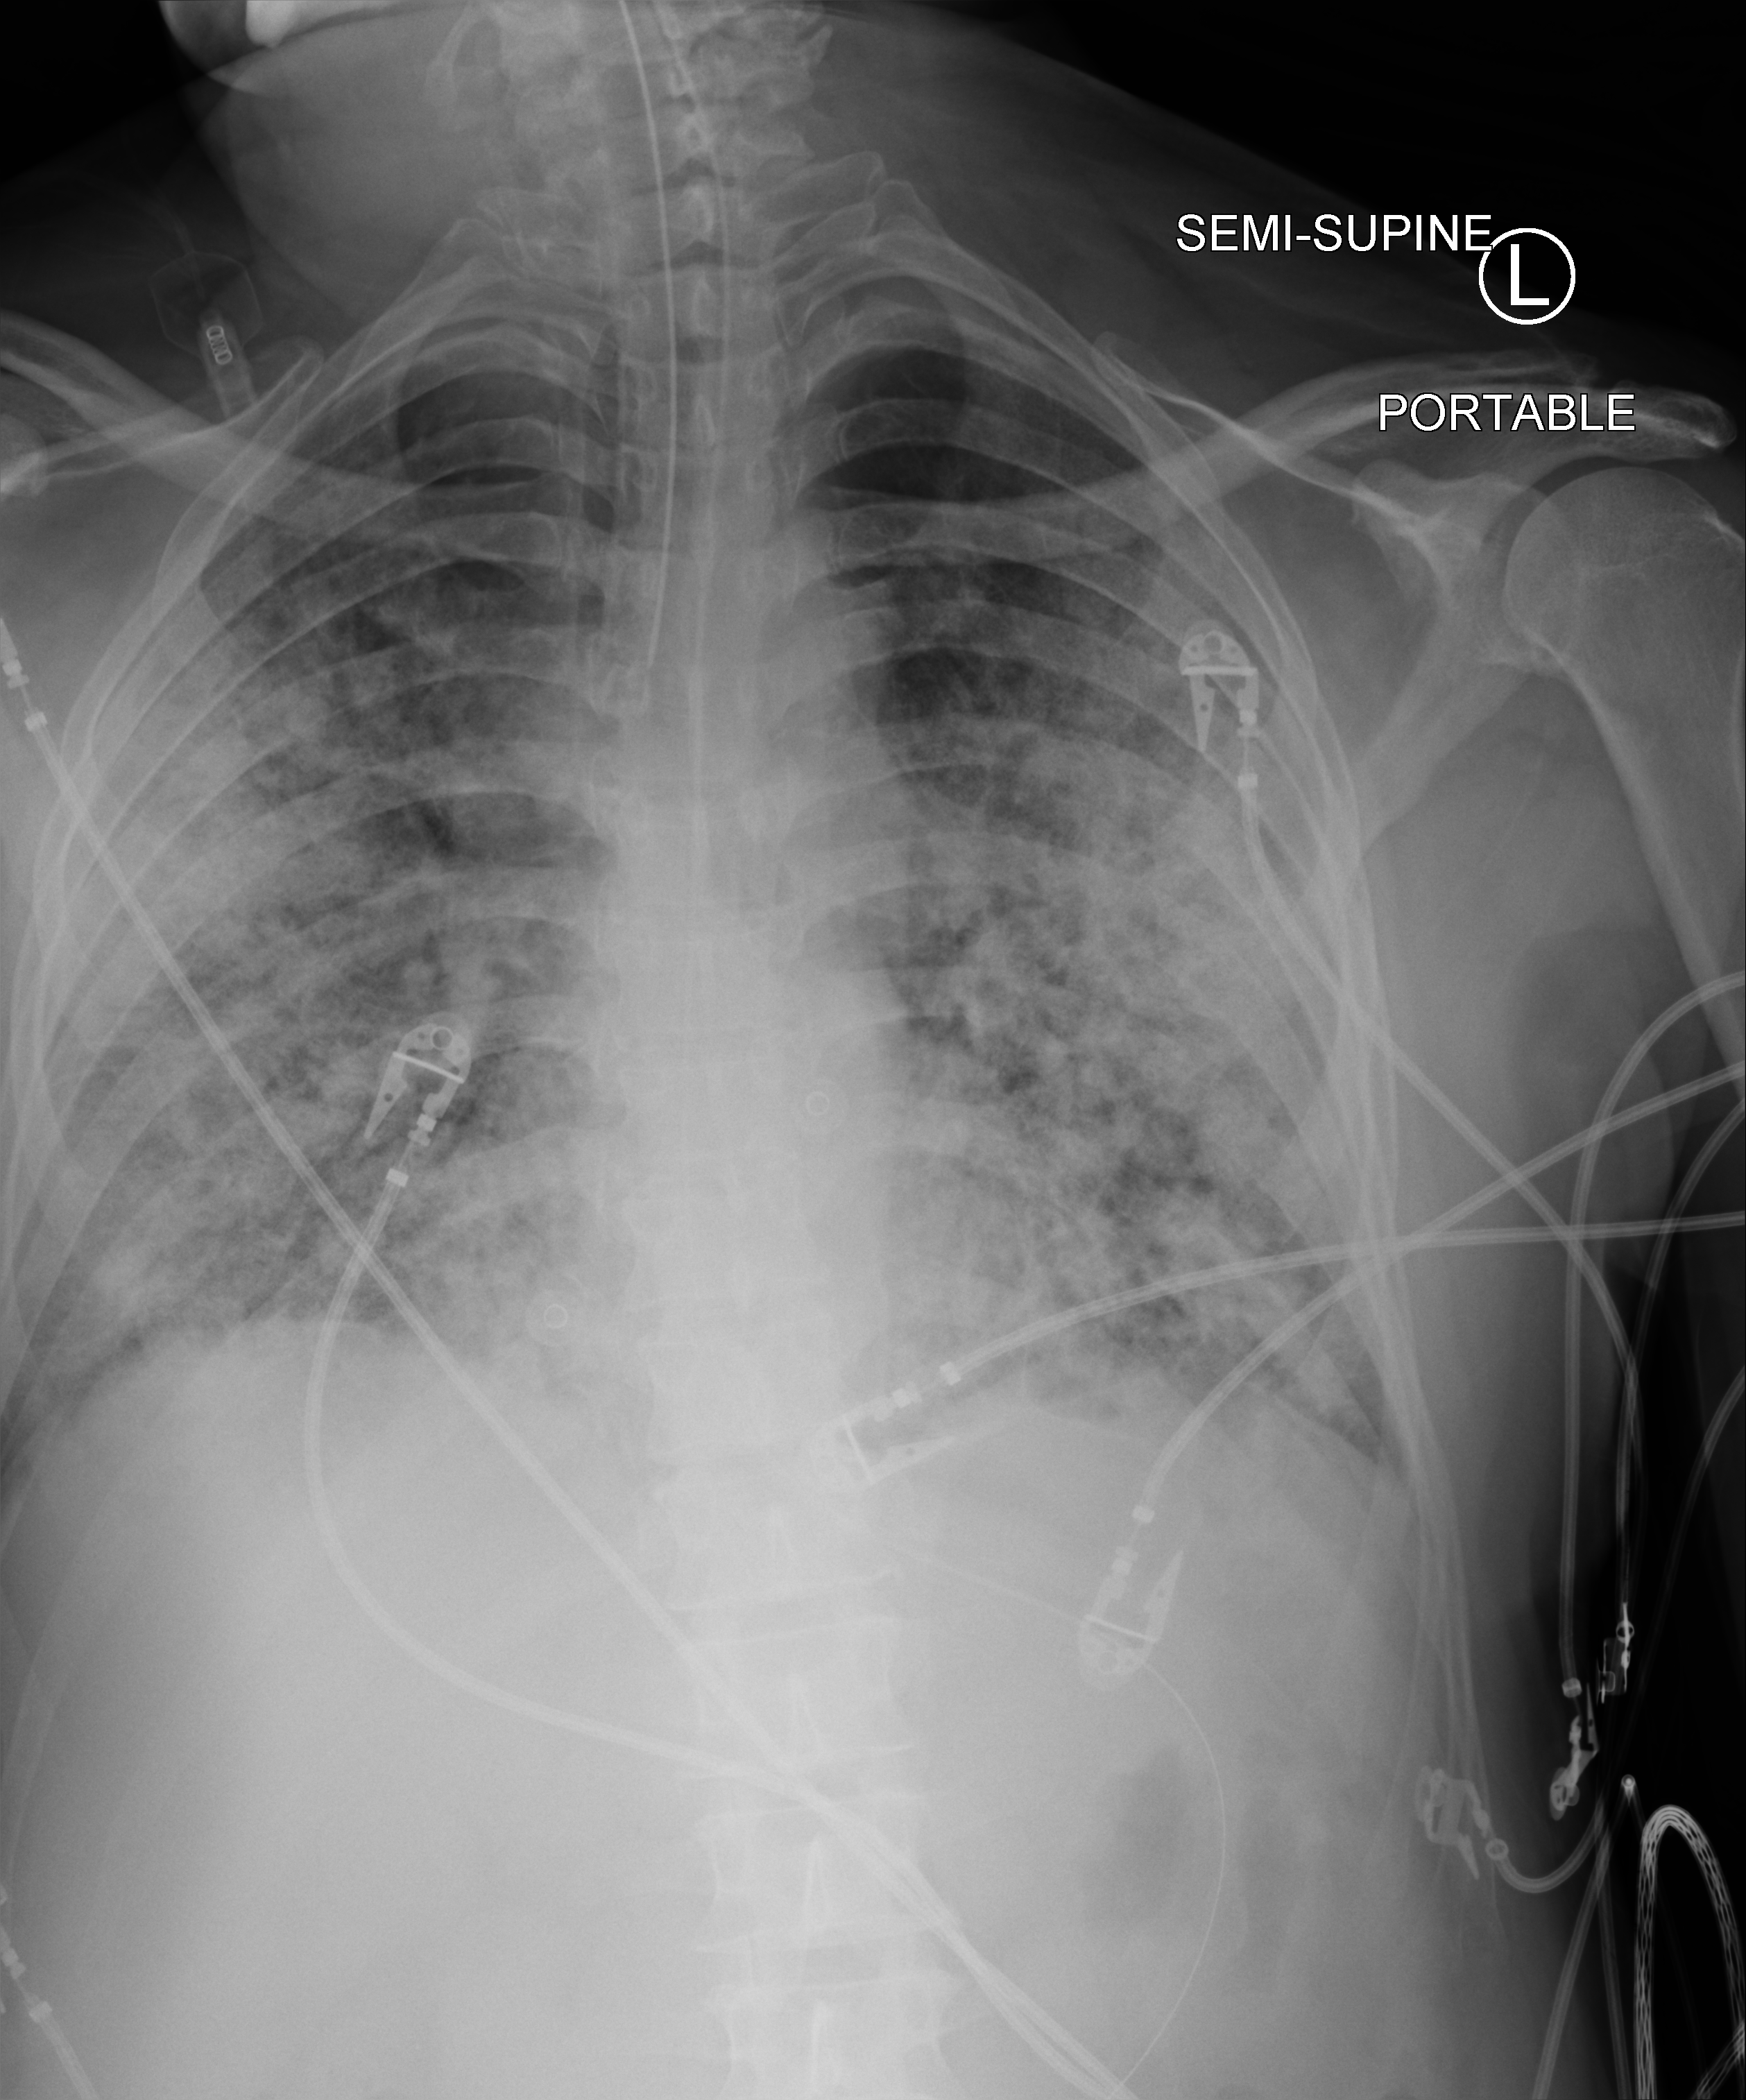
Portable chest radiograph; anteroposterior (AP) projection. Patient hospitalised with COVID-19; male, aged 60–74 years.
Admission-level facts for this patient (not findings on this image; timing relative to this image not recorded):
- admitted to intensive care during this hospital stay: yes
- length of hospital stay: 65 days
- mechanically ventilated during this hospital stay: yes